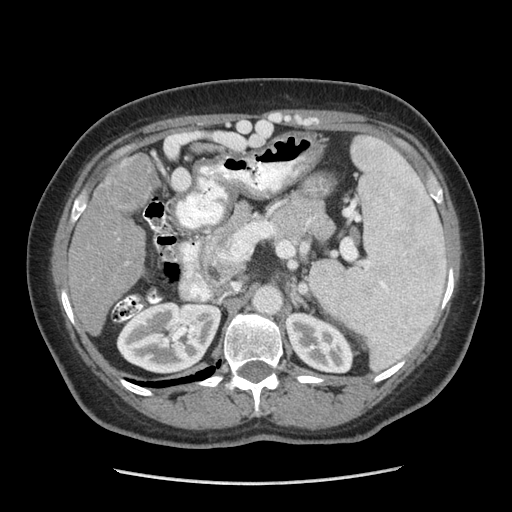
Contrast-enhanced abdominal CT (liver protocol), one axial slice; slice 143 of 185 in the series (ordered by position); 140 kVp; soft-tissue window (W 400 / L 40 HU); 2.5 mm slice thickness; 512 × 512 image matrix. Case-level facts recorded for this patient, not image findings: diagnosis: hepatocellular carcinoma (patient treated with transarterial chemoembolisation; whether this scan precedes or follows treatment is not stated here); TNM stage (as recorded): Stage-I; Child-Pugh class: A; tumour differentiation: poorly differentiated.
Annotated regions visible in this slice (semi-automatically segmented with operator editing):
- liver parenchyma outside the tumour (the mass and vessels are separate outlines, so this box may not span the whole liver): bounding box <68,154,158,334> (left, top, right, bottom; pixels)
- mass: <96,157,159,214>